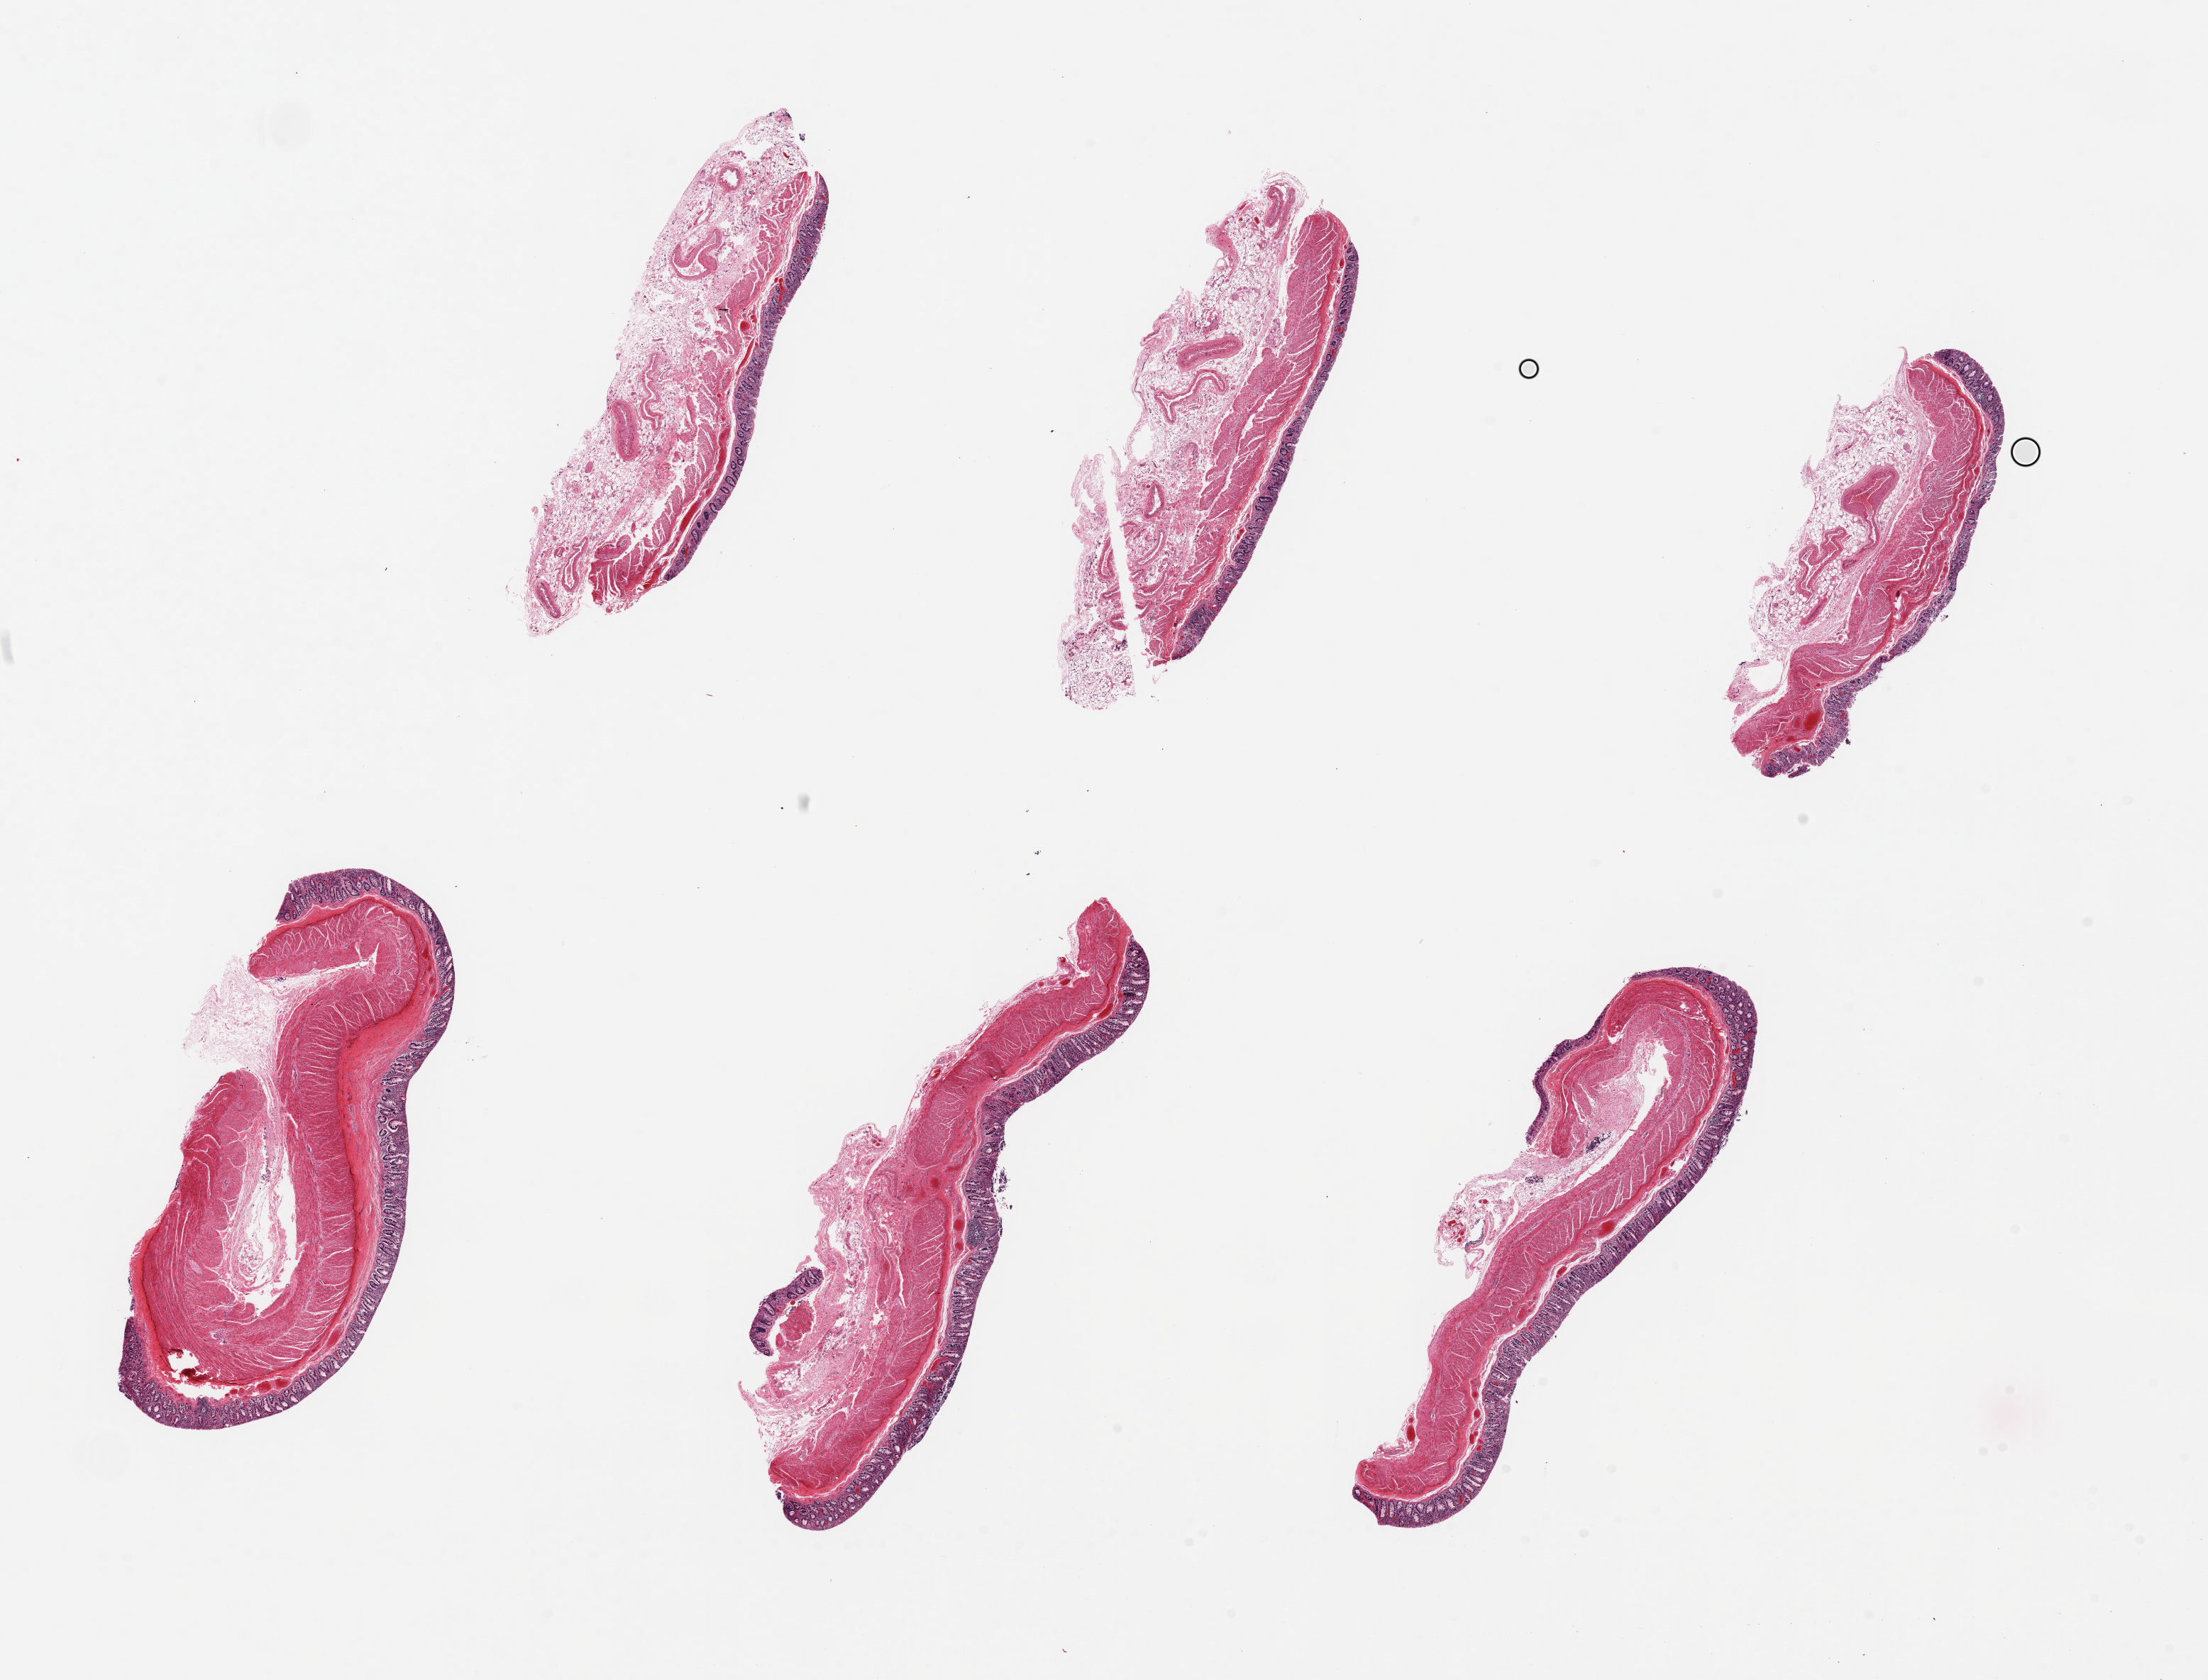
Haematoxylin and eosin whole-slide image — a low-resolution overview of the entire scanned area, about 24.6 x 18.7 mm. PAXgene-fixed, paraffin-embedded tissue. Section of transverse colon (target tissue). Donor tissue sample. Donor sex: male.
Reviewer comment on this tissue sample: 6 pieces, up to 8x2mm; mucosa moderately autolyzed.